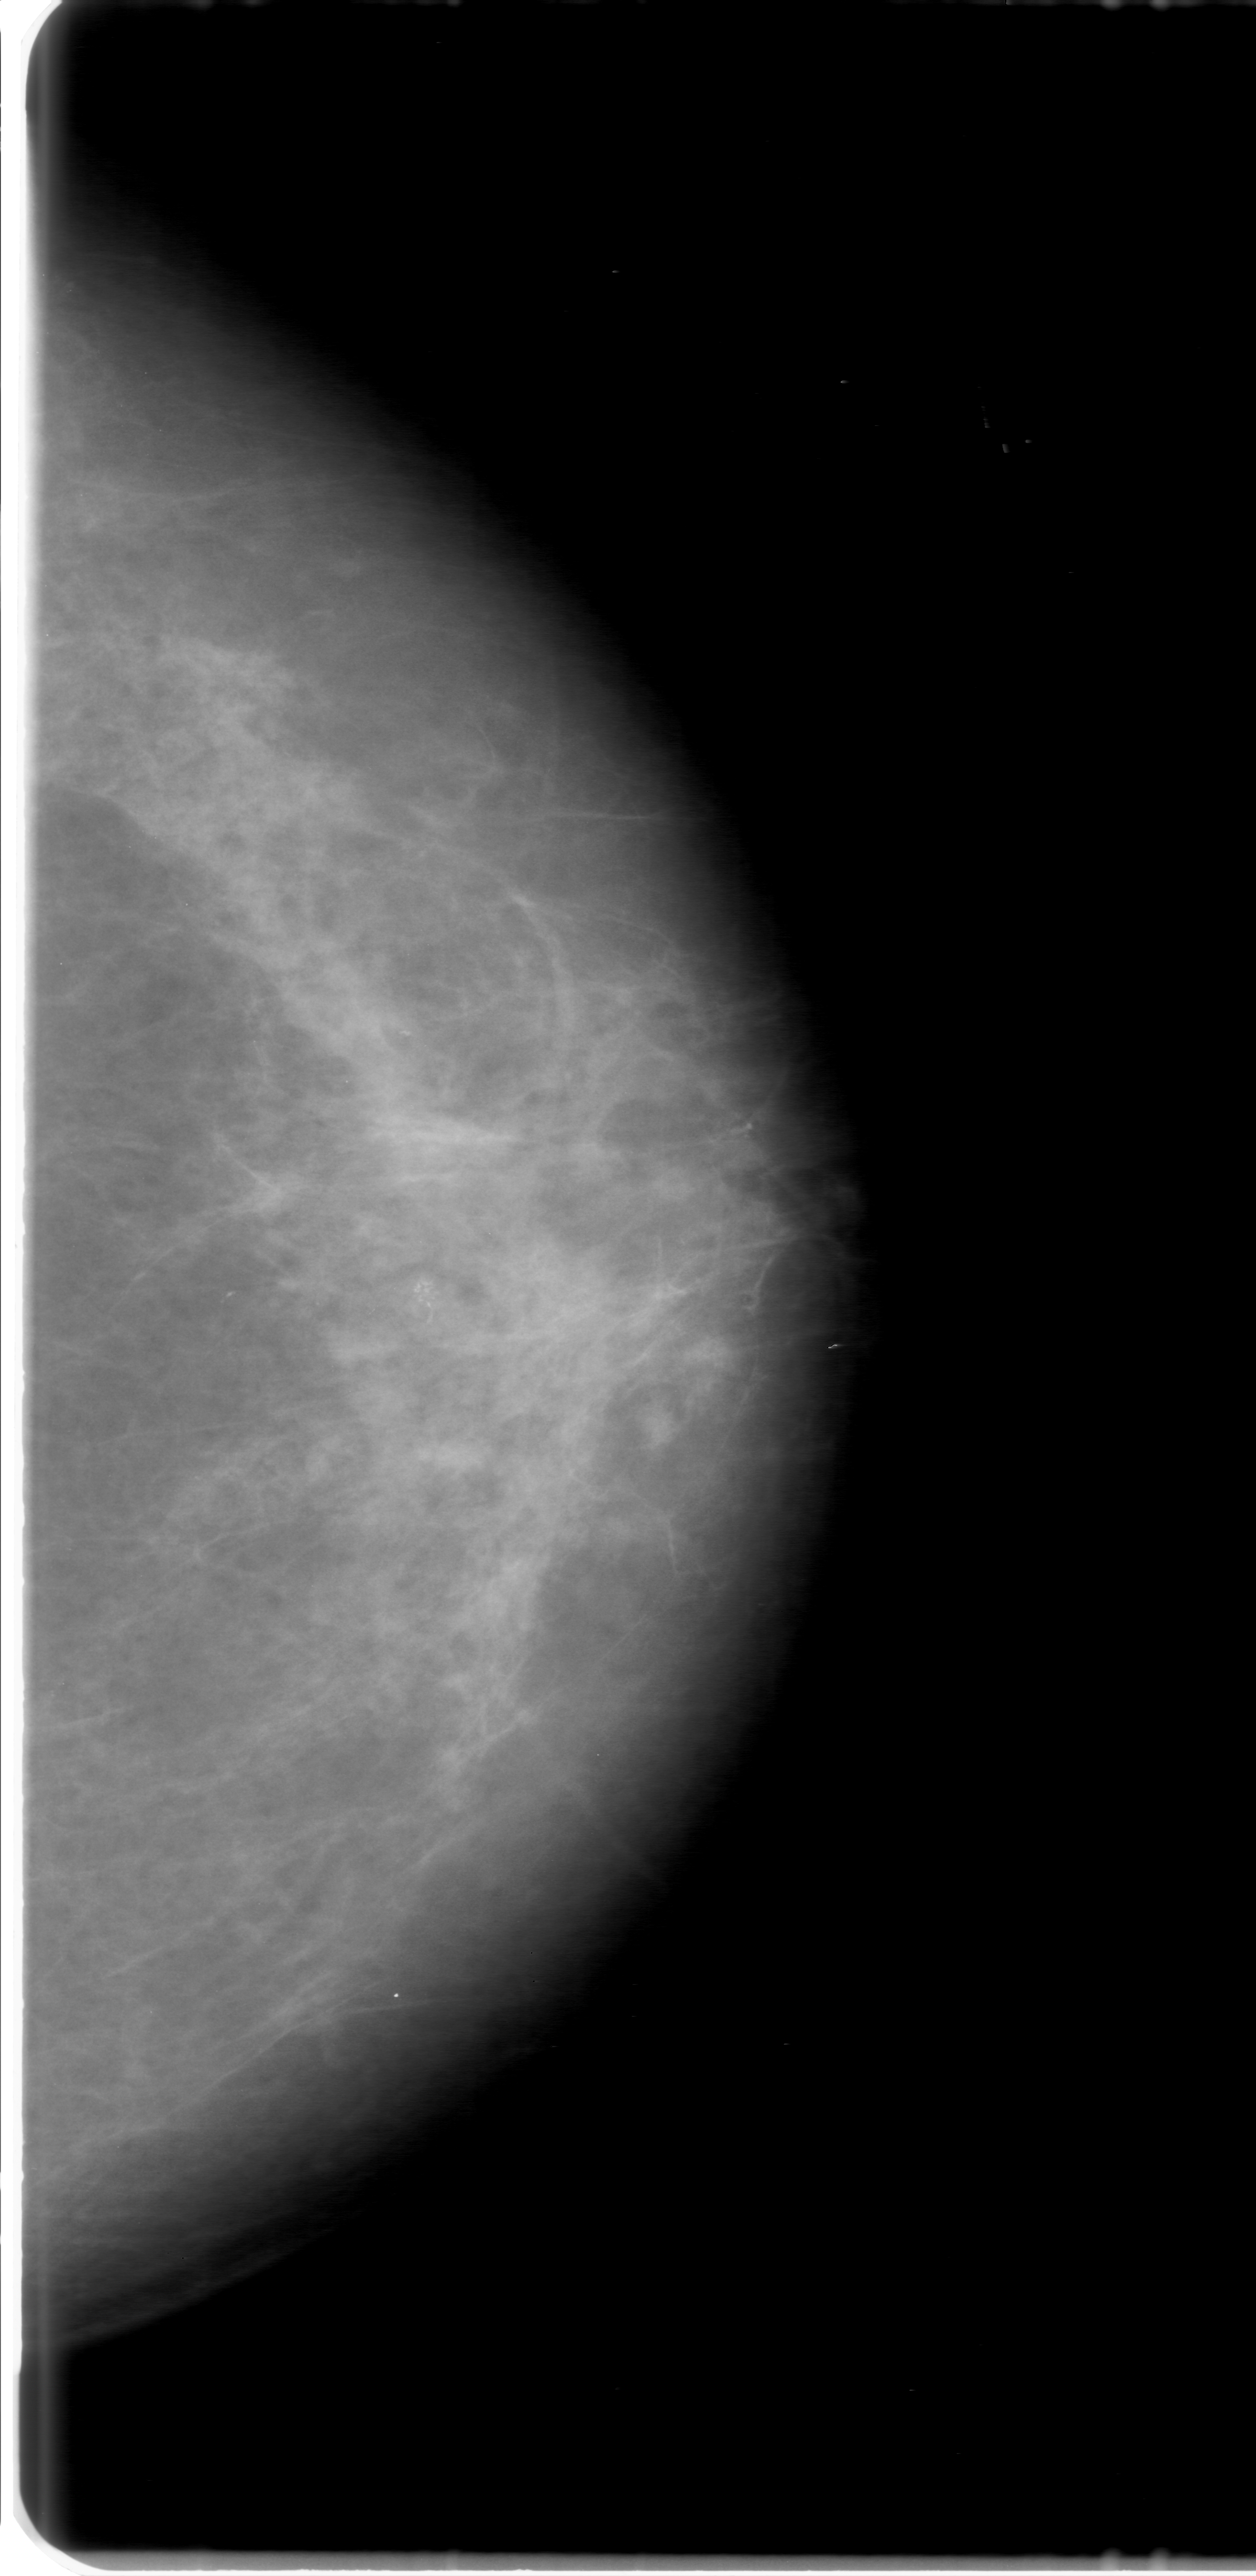
Digitized screen-film mammogram. Left breast. CC view. BI-RADS breast density category 2 (scale 1–4). 1256 × 2576 image matrix.
Expert-marked regions of interest on this film, with their recorded descriptors:
- calcifications, morphology pleomorphic, distribution clustered; BI-RADS assessment category 3; pathology (as recorded): malignant: bounding box [x1, y1, x2, y2] px = [287, 1175, 572, 1458]